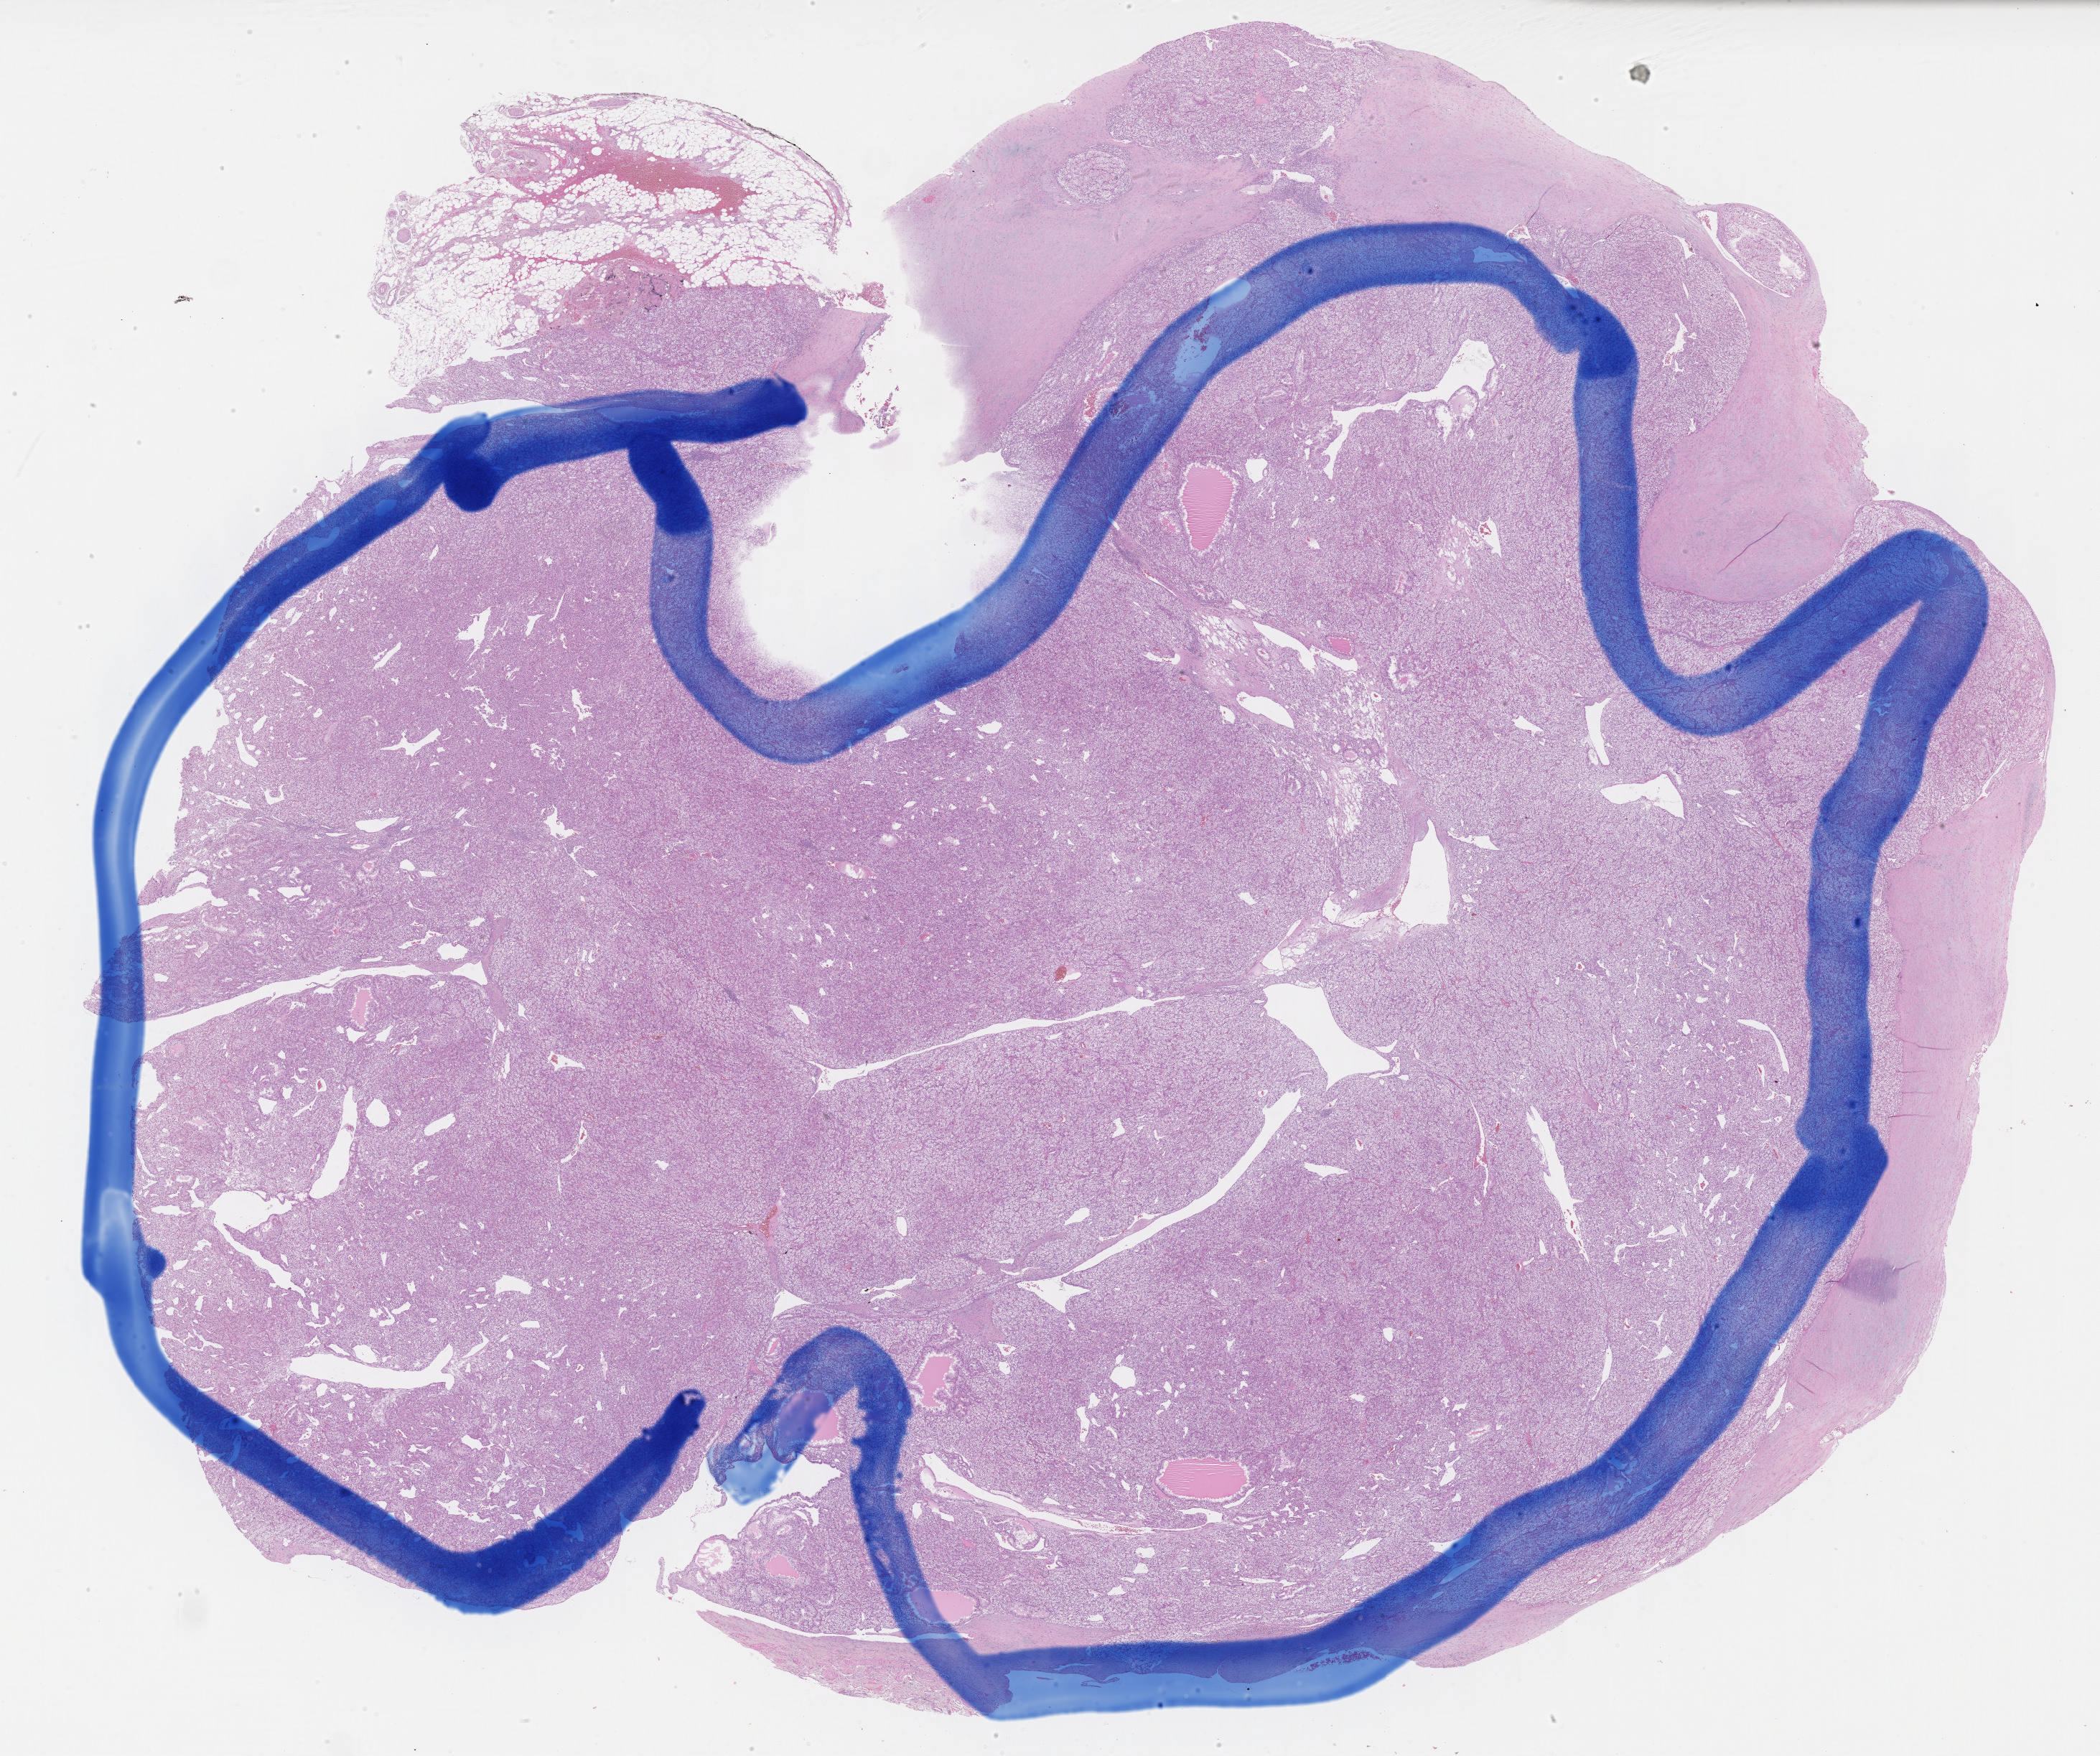
Hematoxylin and eosin (H&E) stained whole-slide image — shown as a low-resolution overview of the whole scanned area (about 23.6 x 19.8 mm, from a 40x scan). Formalin-fixed paraffin-embedded (FFPE) diagnostic section. Kidney, primary tumour sample. Patient: male, age at initial diagnosis 58 years. Histologic grade: G3 (poorly differentiated).
Laterality: right. AJCC pathologic stage: III. Diagnosis: Clear cell adenocarcinoma, NOS.